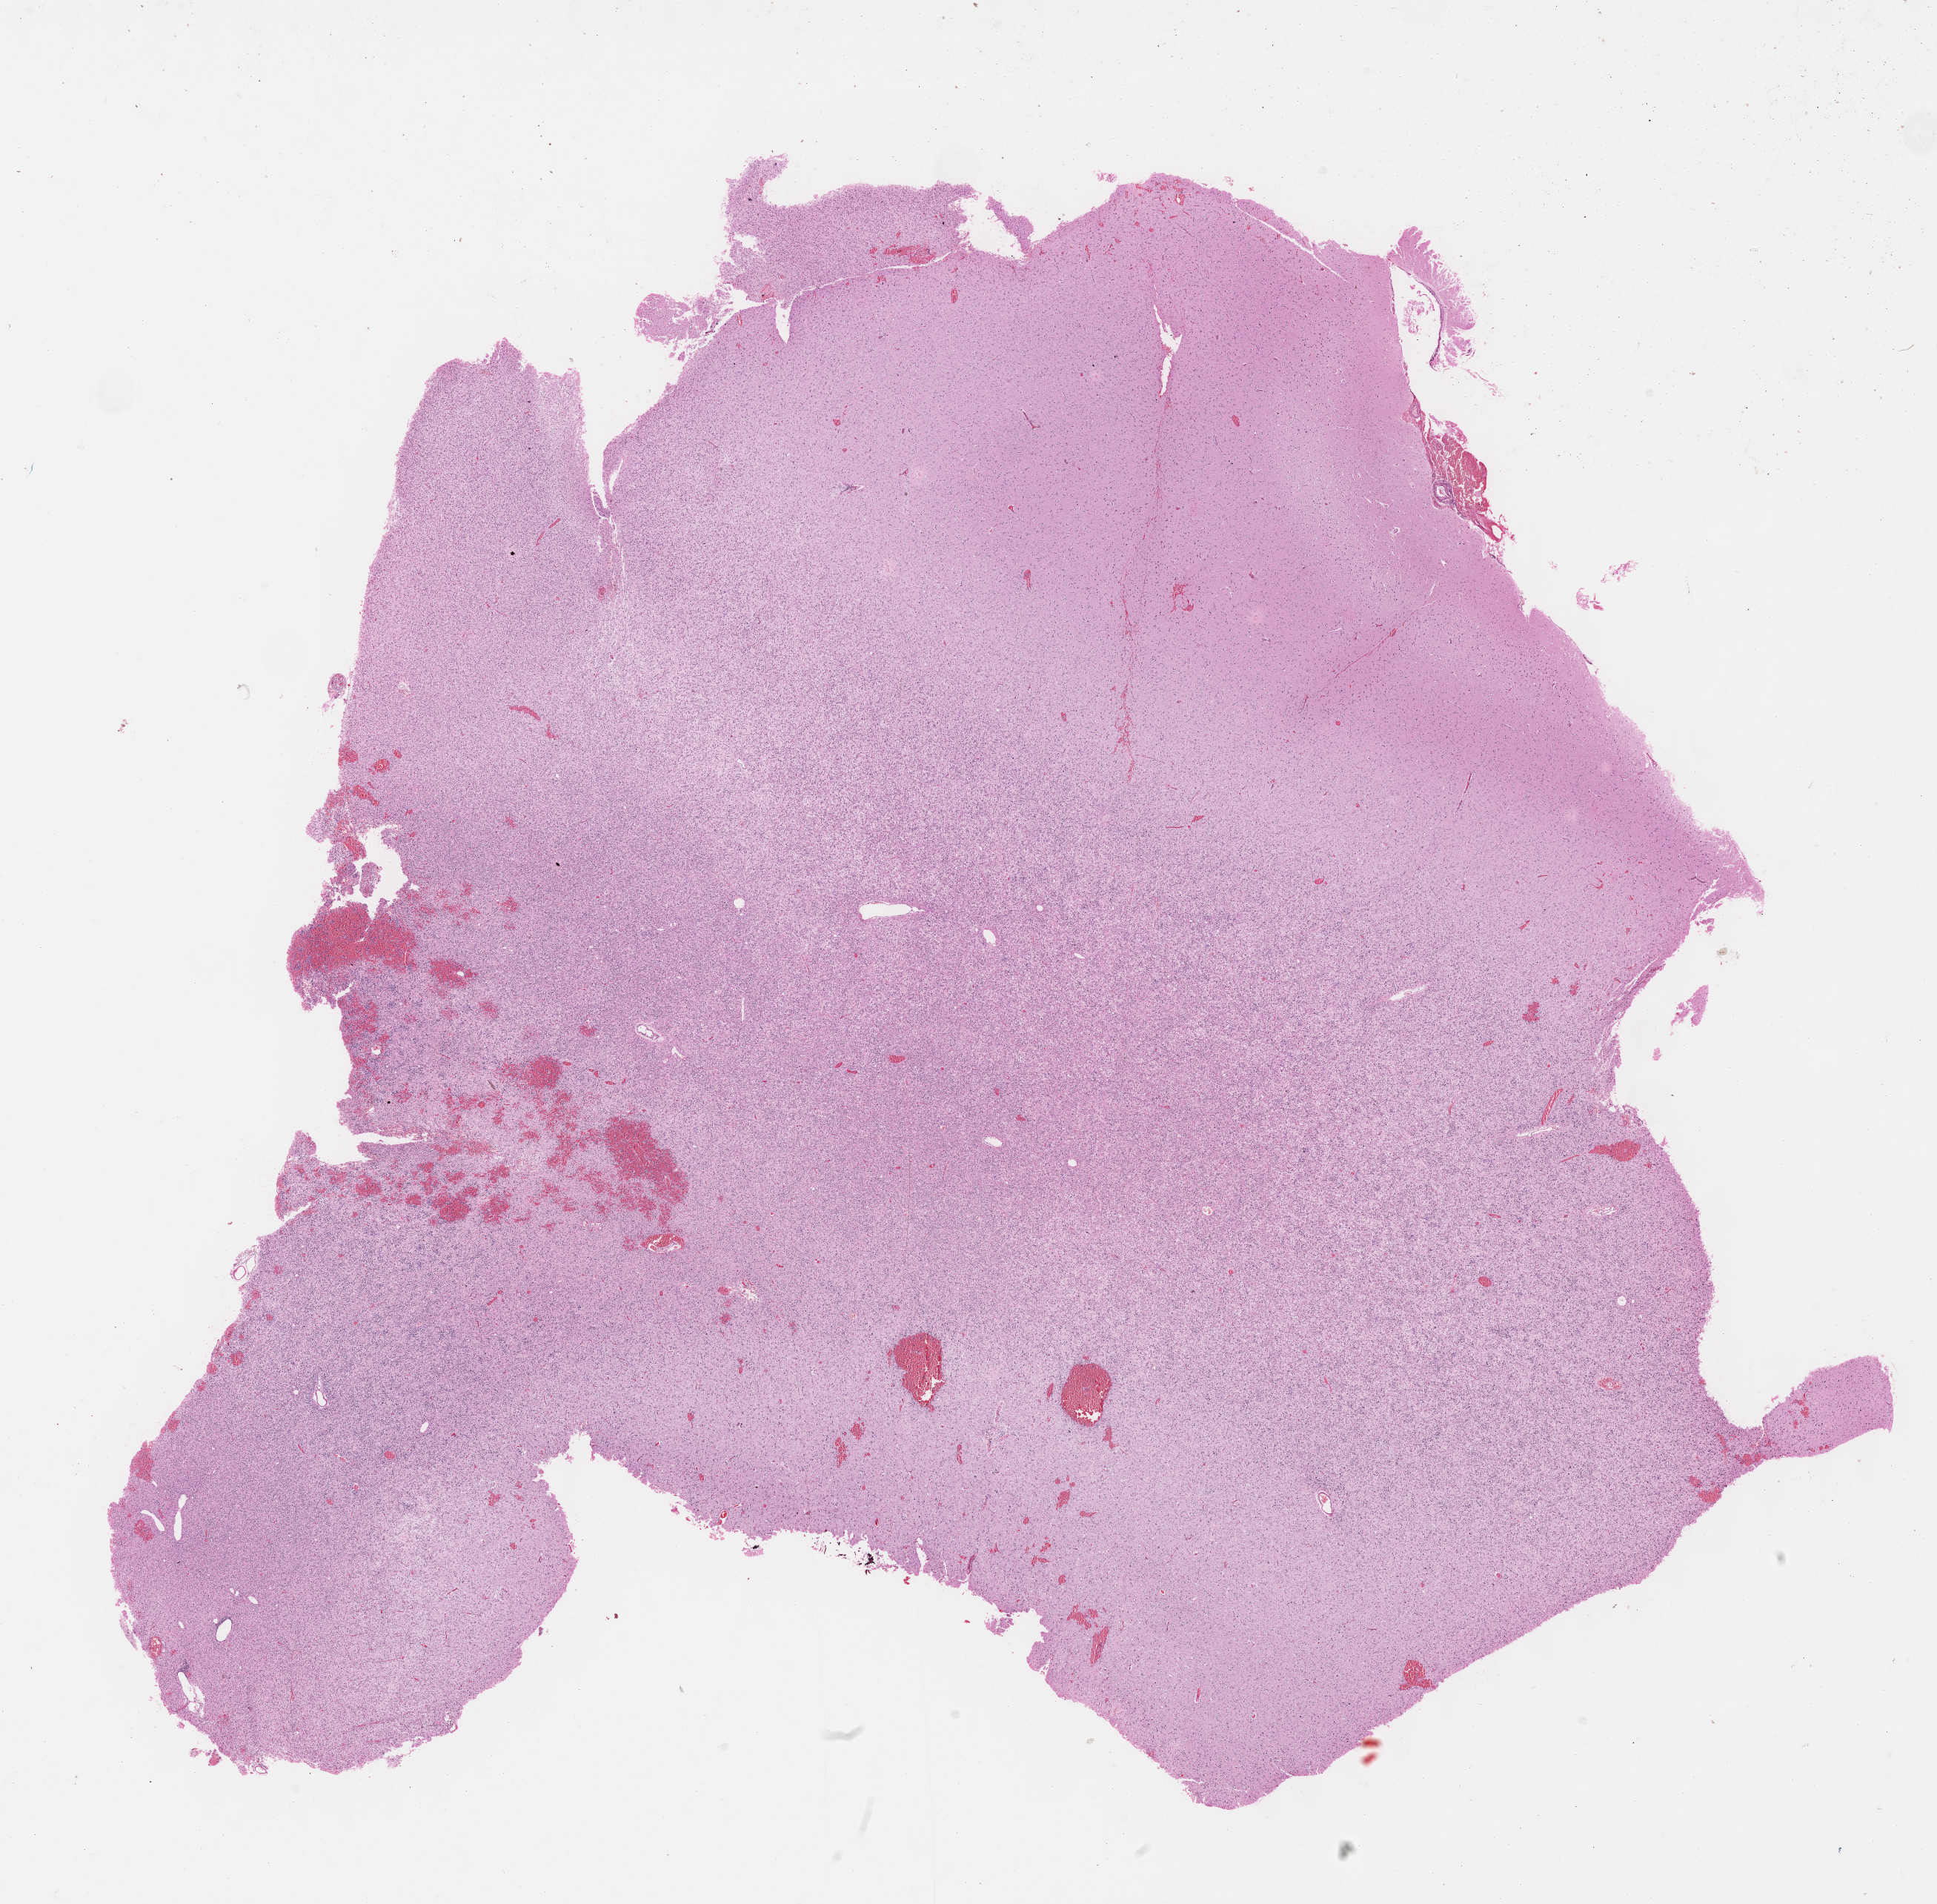
Whole-slide histology image, H&E, shown as a low-resolution overview of the whole scanned area (about 21.1 x 20.8 mm); formalin-fixed paraffin-embedded (FFPE) diagnostic section; primary tumour sample from the brain. Male, age 32 years at initial diagnosis.
Pathologic diagnosis: Mixed glioma.